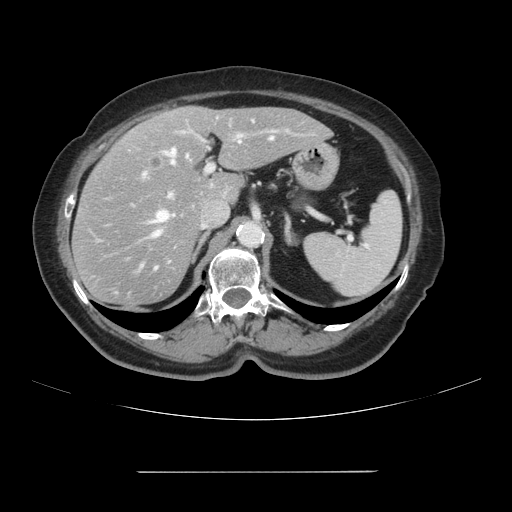
Contrast-enhanced abdominal CT, one axial slice; position 65 of 111 along the scan axis; 120 kVp; soft-tissue window (W 400 / L 40 HU); 512 × 512 image matrix. Female patient, age 74 years. From the clinical record (not read from this slice): diagnosis: colorectal cancer liver metastases, imaged before liver resection; multiple liver metastases: yes; largest metastasis: 1.1 cm; disease in both lobes: yes.
Annotated regions visible in this slice (manually delineated by an expert):
- hepatic veins: box from (x=139, y=137) to (x=274, y=265) px
- liver: (x=74, y=107)–(x=330, y=307)
- planned liver remnant (the part of the liver to remain after resection): (x=148, y=107)–(x=330, y=203)
- portal vein (with intrahepatic branches): (x=141, y=117)–(x=317, y=200)
- liver metastasis: (x=151, y=158)–(x=160, y=165)